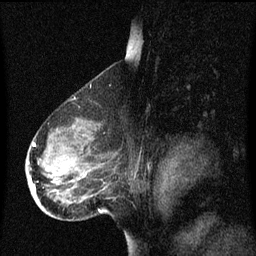
Breast MRI (dynamic contrast-enhanced), one sagittal slice; slice 44 of 60 in the series (ordered by position); dynamic contrast-enhanced series, image 2 of 3 at this slice position (ordered by acquisition); 1.5 T; TE 4.2 ms, TR 8.4 ms; 256 × 256 image matrix. Female patient, age 49 years. From the clinical record (not read from this slice): setting: breast cancer imaged before/during neoadjuvant chemotherapy; receptor status: HR-positive, HER2-negative.
Annotated regions visible in this slice (semi-automatic segmentation, software-assisted and operator-edited):
- analysis volume of interest (the breast-tissue region the enhancement analysis was run in; not a lesion): bounding box <27,126,106,201> (left, top, right, bottom; pixels)
- tumour enhancement mask (voxels above the 70 % enhancement threshold inside the analysis volume of interest): <33,144,37,191>